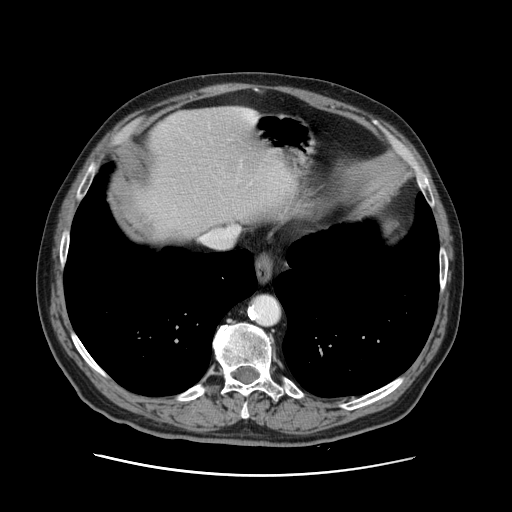
Contrast-enhanced abdominal CT, one axial slice; slice 113 of 141 in the series (ordered by position); 120 kVp; soft-tissue window (W 400 / L 40 HU); 2.5 mm slice thickness; 512 × 512 image matrix, field of view 395 × 395 mm. Male patient, age 72 years. Case-level facts recorded for this patient, not image findings: diagnosis: colorectal cancer liver metastases, imaged before liver resection; multiple liver metastases: yes; largest metastasis: 5.4 cm; disease in both lobes: yes.
Outlined on this slice (outlined manually by an expert reader):
- liver: bounding box [x1, y1, x2, y2] px = [133, 107, 283, 239]
- planned liver remnant (the part of the liver to remain after resection): [151, 107, 282, 240]